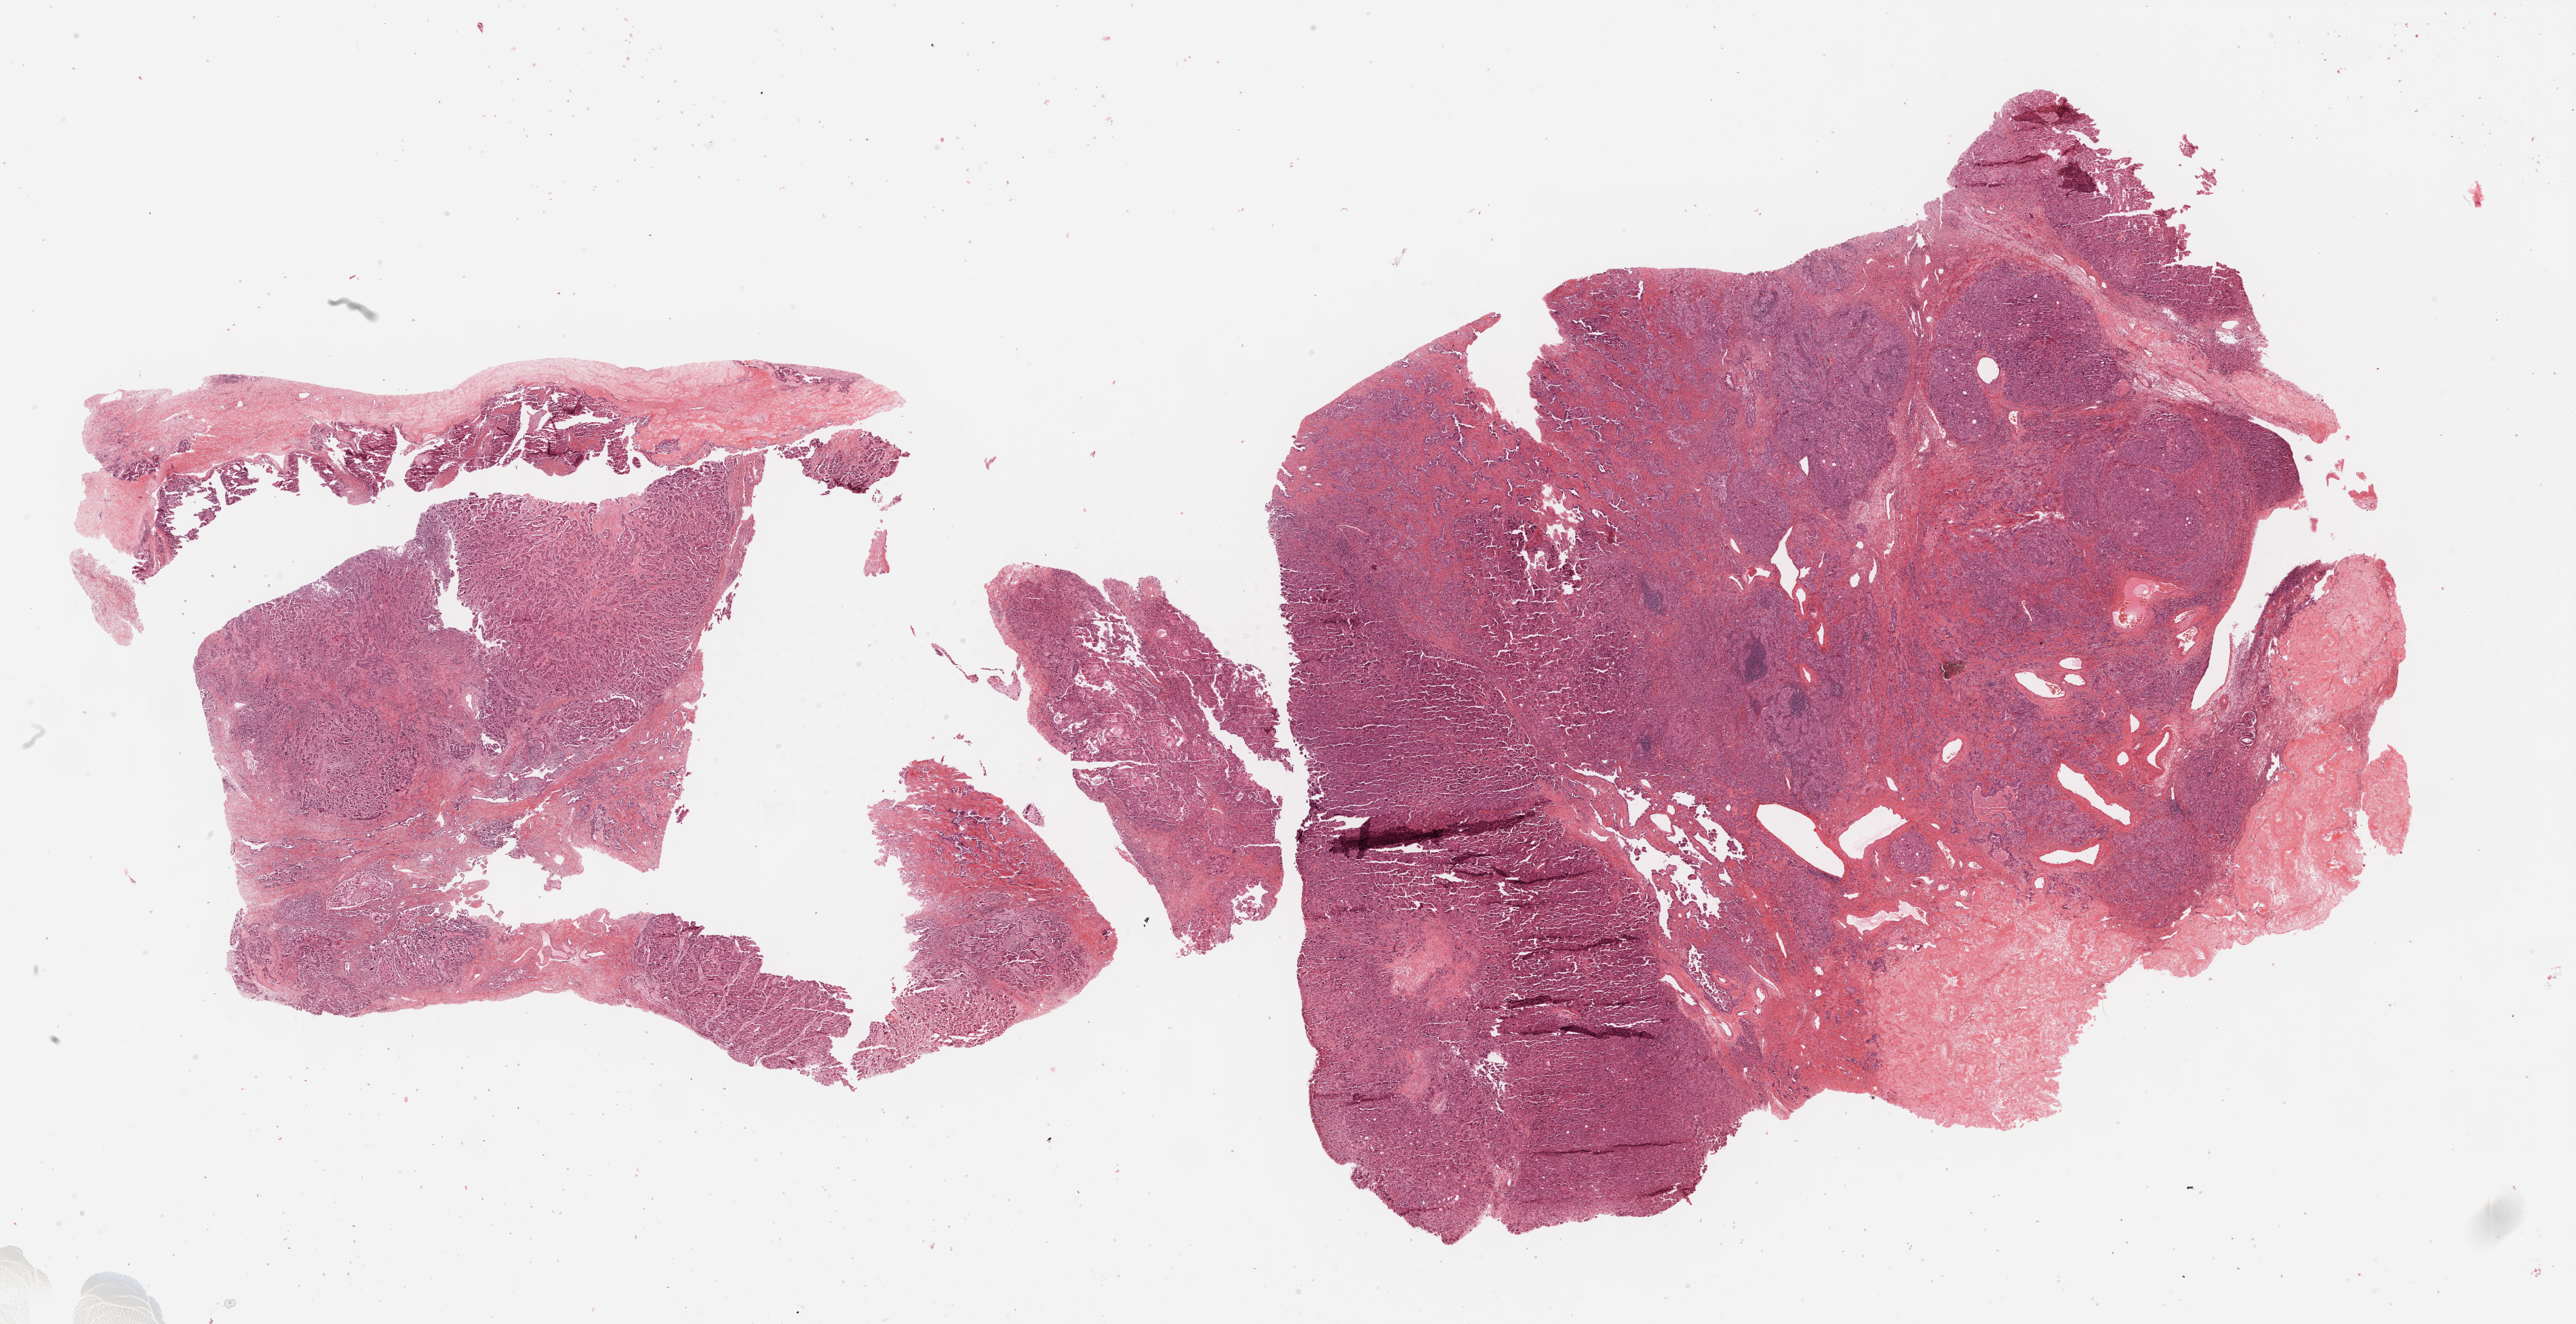
Digitized Hematoxylin and eosin (H&E) stained tissue section (whole slide) — low-resolution overview of the scanned area, about 30.7 x 15.8 mm (slide scanned at 40x); formalin-fixed paraffin-embedded (FFPE) diagnostic section; ovary, primary tumour sample. Female, age 75 years at initial diagnosis. Histologic grade: G3 (poorly differentiated).
FIGO stage: IV. Pathologic diagnosis: Serous cystadenocarcinoma, NOS.